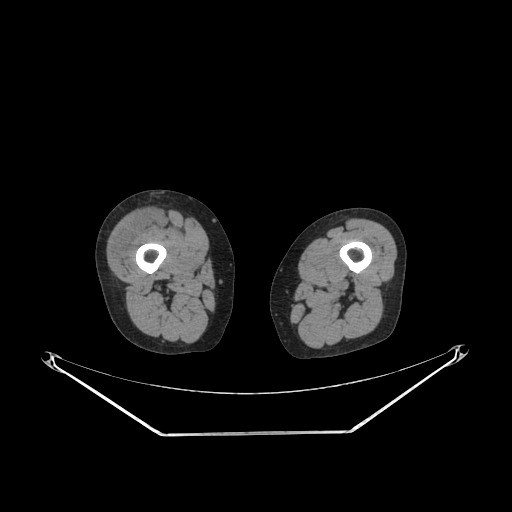
CT of an extremity soft-tissue mass (from a PET/CT study), one axial slice; slice 213 of 311 in the series (ordered by position); soft-tissue window (W 400 / L 40 HU); 3.75 mm slice thickness; 512 × 512 image matrix. Female patient. Case-level facts recorded for this patient, not image findings: histological type: pleiomorphic undifferentiated sarcoma; grade: high; site of the primary tumour: right quadricep.
Annotated regions visible in this slice (expert contour drawn on MRI and transferred to this co-registered scan by the dataset authors):
- tumour plus oedema (research contour): bounding box (x1, y1, x2, y2) in pixels: (110, 210, 163, 261)